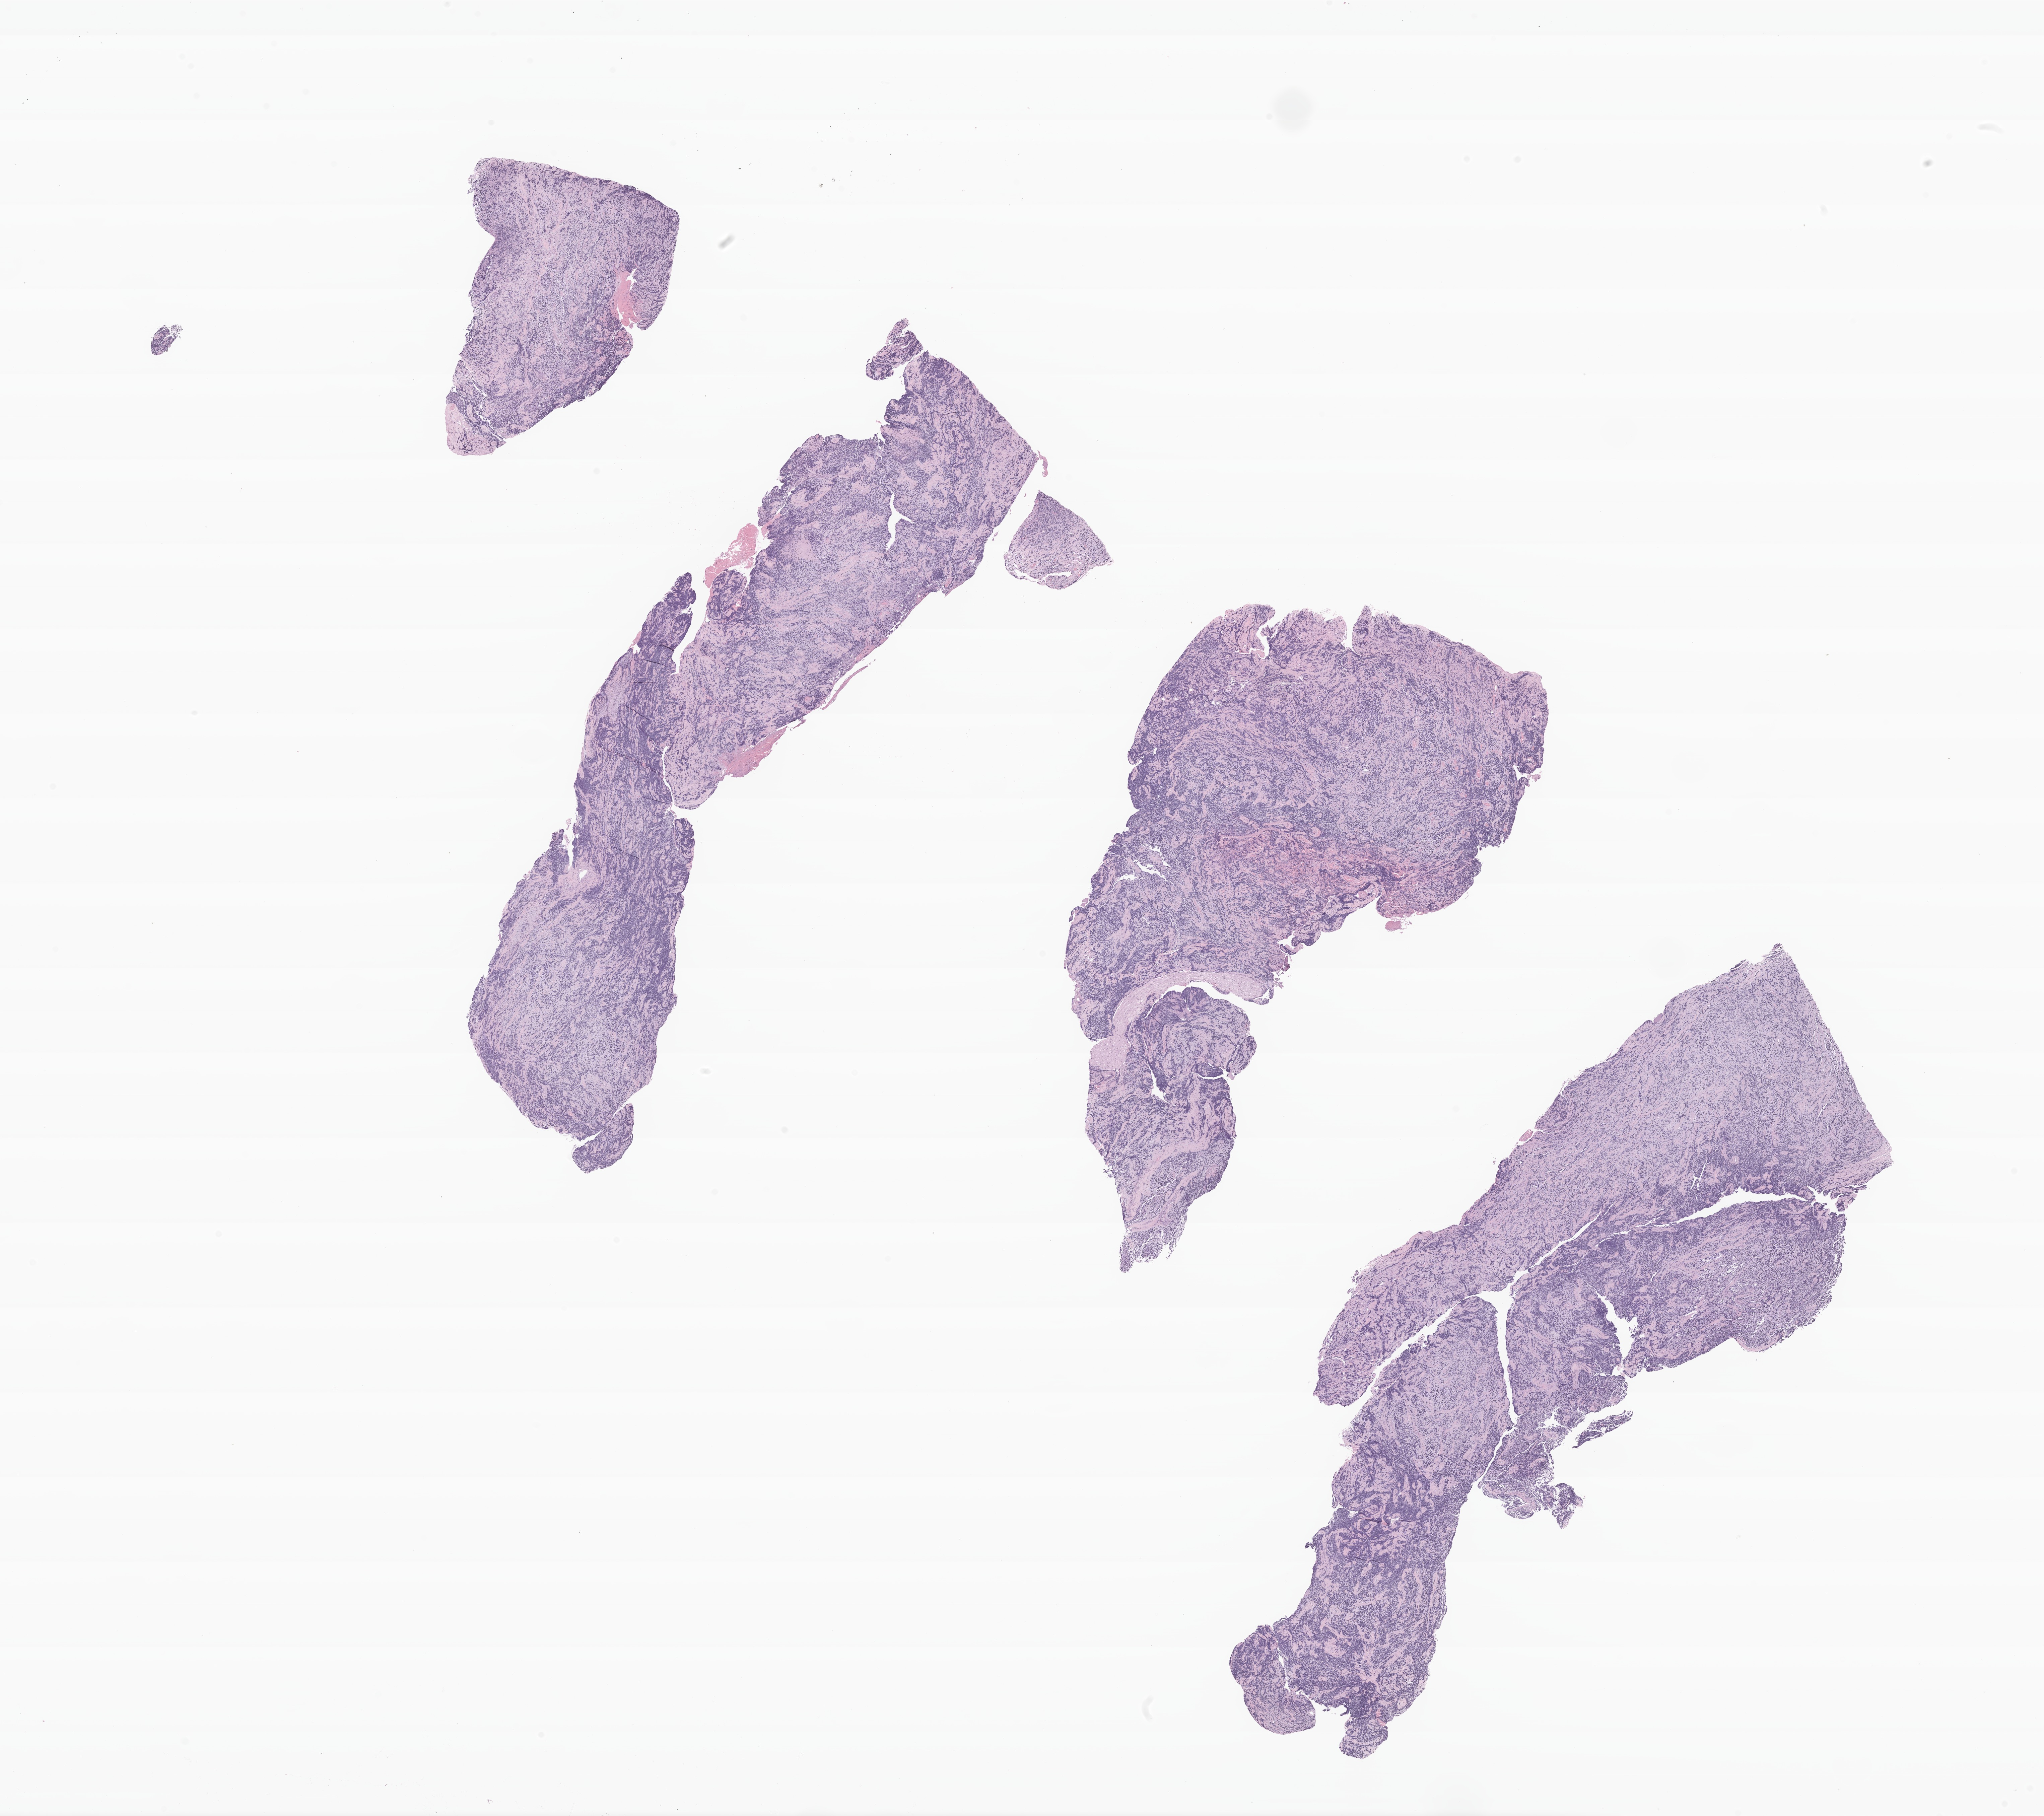
Hematoxylin and eosin (H&E) whole-slide image of tumor tissue from the brain — shown as a low-resolution overview of the whole scanned area (about 25.7 x 22.8 mm). Patient female; age 207 months.
- specimen: FFPE section